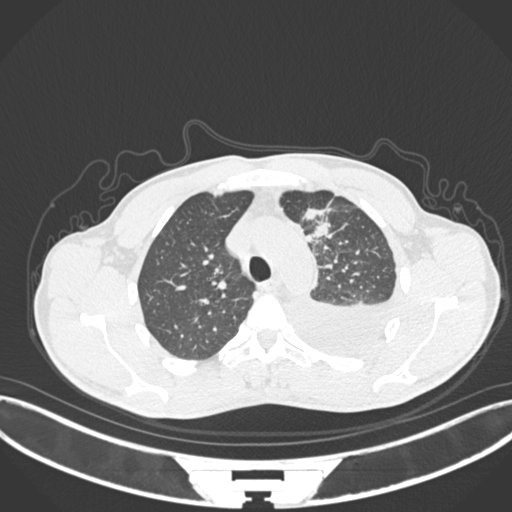
Chest CT, one axial slice; 120 kVp; lung window (W 1500 / L -600 HU); 1 mm slice thickness; 512 × 512 image matrix, field of view 400 × 400 mm. Patient: male, 49 years. Case-level facts recorded for this patient, not image findings: clinical TNM (as recorded): T1c N1 M1.
Outlined on this slice (rectangle marked by the reading radiologist):
- lung tumour (recorded histology: adenocarcinoma): bounding box (x1, y1, x2, y2) in pixels: (298, 204, 340, 246)